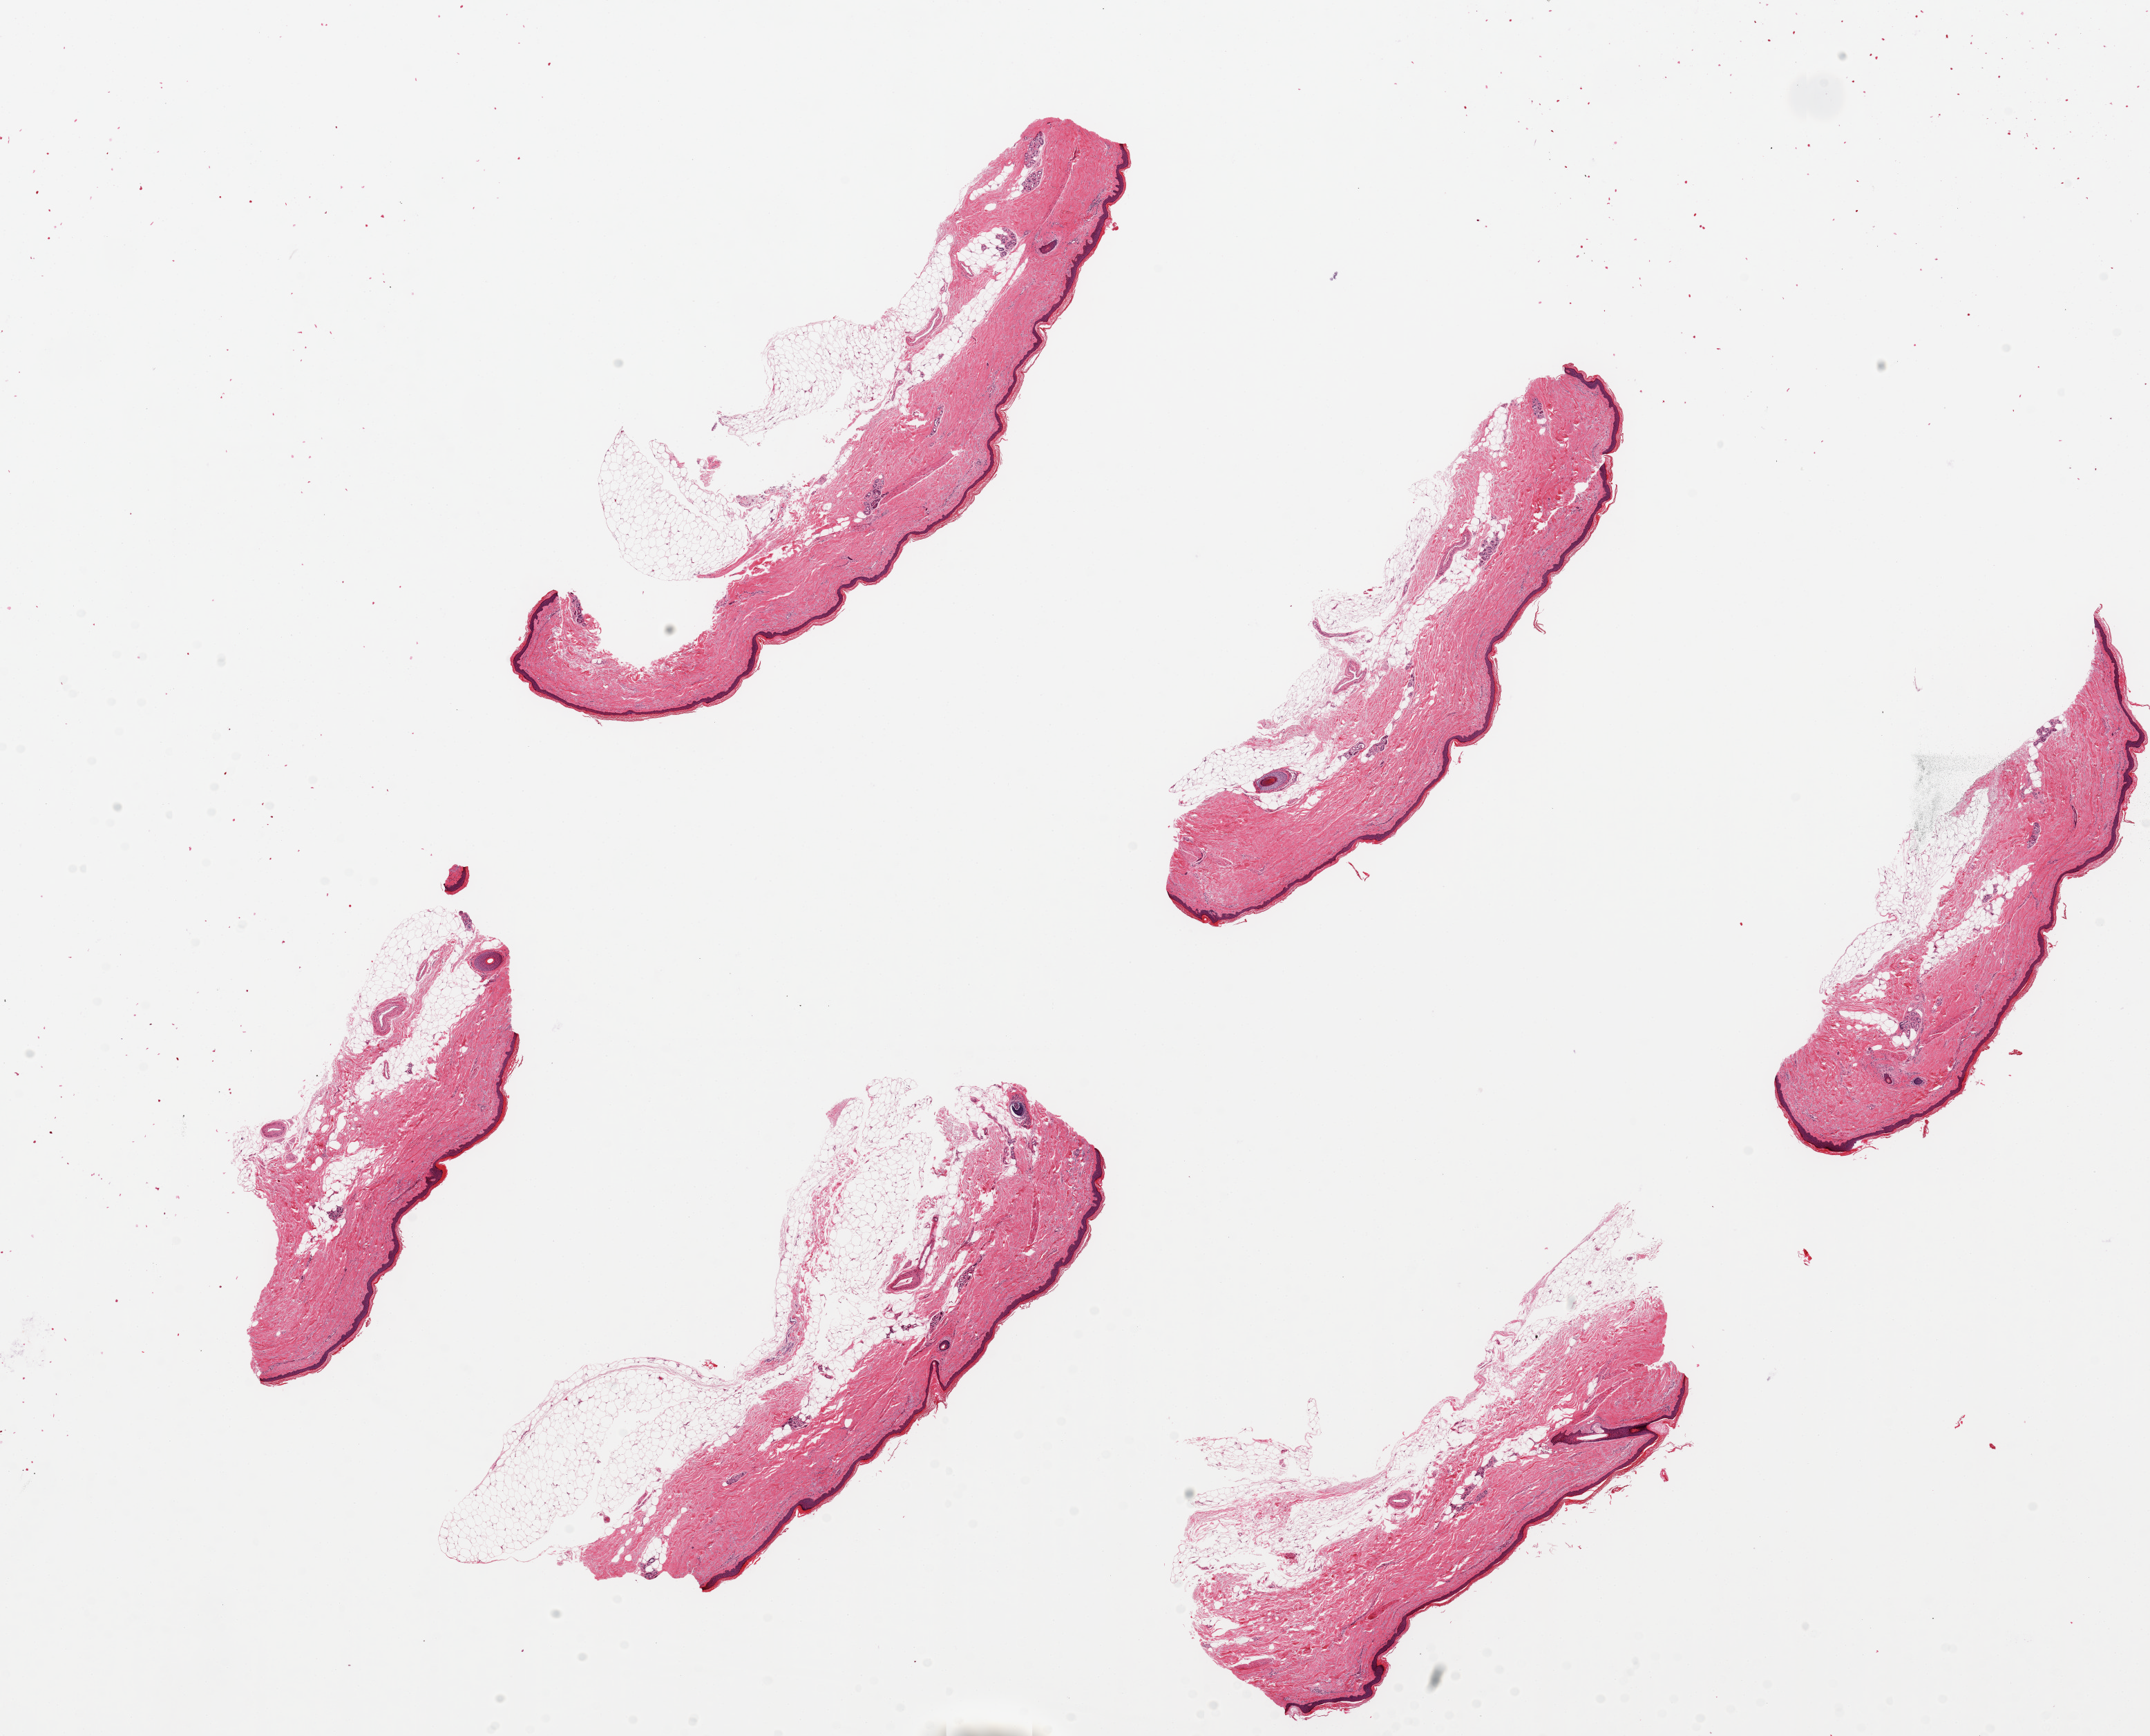
Haematoxylin and eosin whole-slide image, brightfield — low-resolution overview of the scanned area, about 24.6 x 19.9 mm (acquisition: 20x scan); PAXgene-fixed paraffin-embedded (PFPE) section; target tissue: skin of lower leg; donor tissue sample.
Reviewer comment on this tissue sample: 6 pieces ~8x2mm. Squamous epithelium is ~2-3% of thickness.